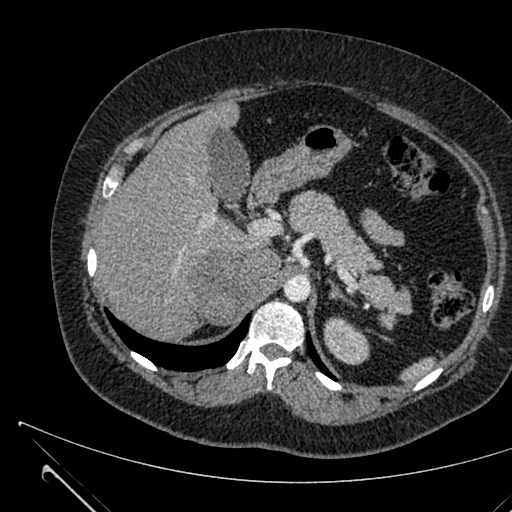
Contrast-enhanced abdominal CT, one axial slice. Slice 452 of 731 in the series (ordered by position). Intravenous contrast given. Soft-tissue window (W 400 / L 40 HU). 512 × 512 image matrix. Patient: female, 36 years. From the clinical record (not read from this slice): diagnosis: adrenocortical carcinoma; tumour side: right adrenal; tumour size at pathology: 10 cm; Ki-67 index: 20 %; stage (as recorded): 4.
Annotated regions visible in this slice (semi-automatically segmented with operator editing):
- mass: bounding box [x1, y1, x2, y2] px = [187, 251, 277, 321]